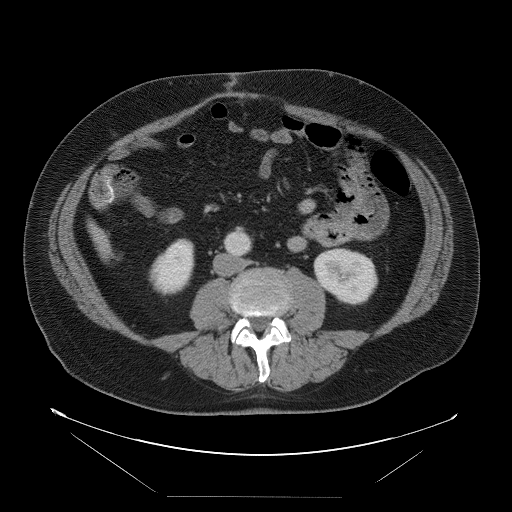
Contrast-enhanced abdominal CT, one axial slice. Position 12 of 114 along the scan axis. Intravenous contrast given. Soft-tissue window (W 400 / L 40 HU). 512 × 512 image matrix. Male patient, age 61 years. From the clinical record (not read from this slice): diagnosis: colorectal cancer liver metastases, imaged before liver resection; multiple liver metastases: no; largest metastasis: 6.5 cm.
Annotated regions visible in this slice (manually delineated by an expert):
- liver: bounding box (x1, y1, x2, y2) in pixels: (92, 230, 109, 257)